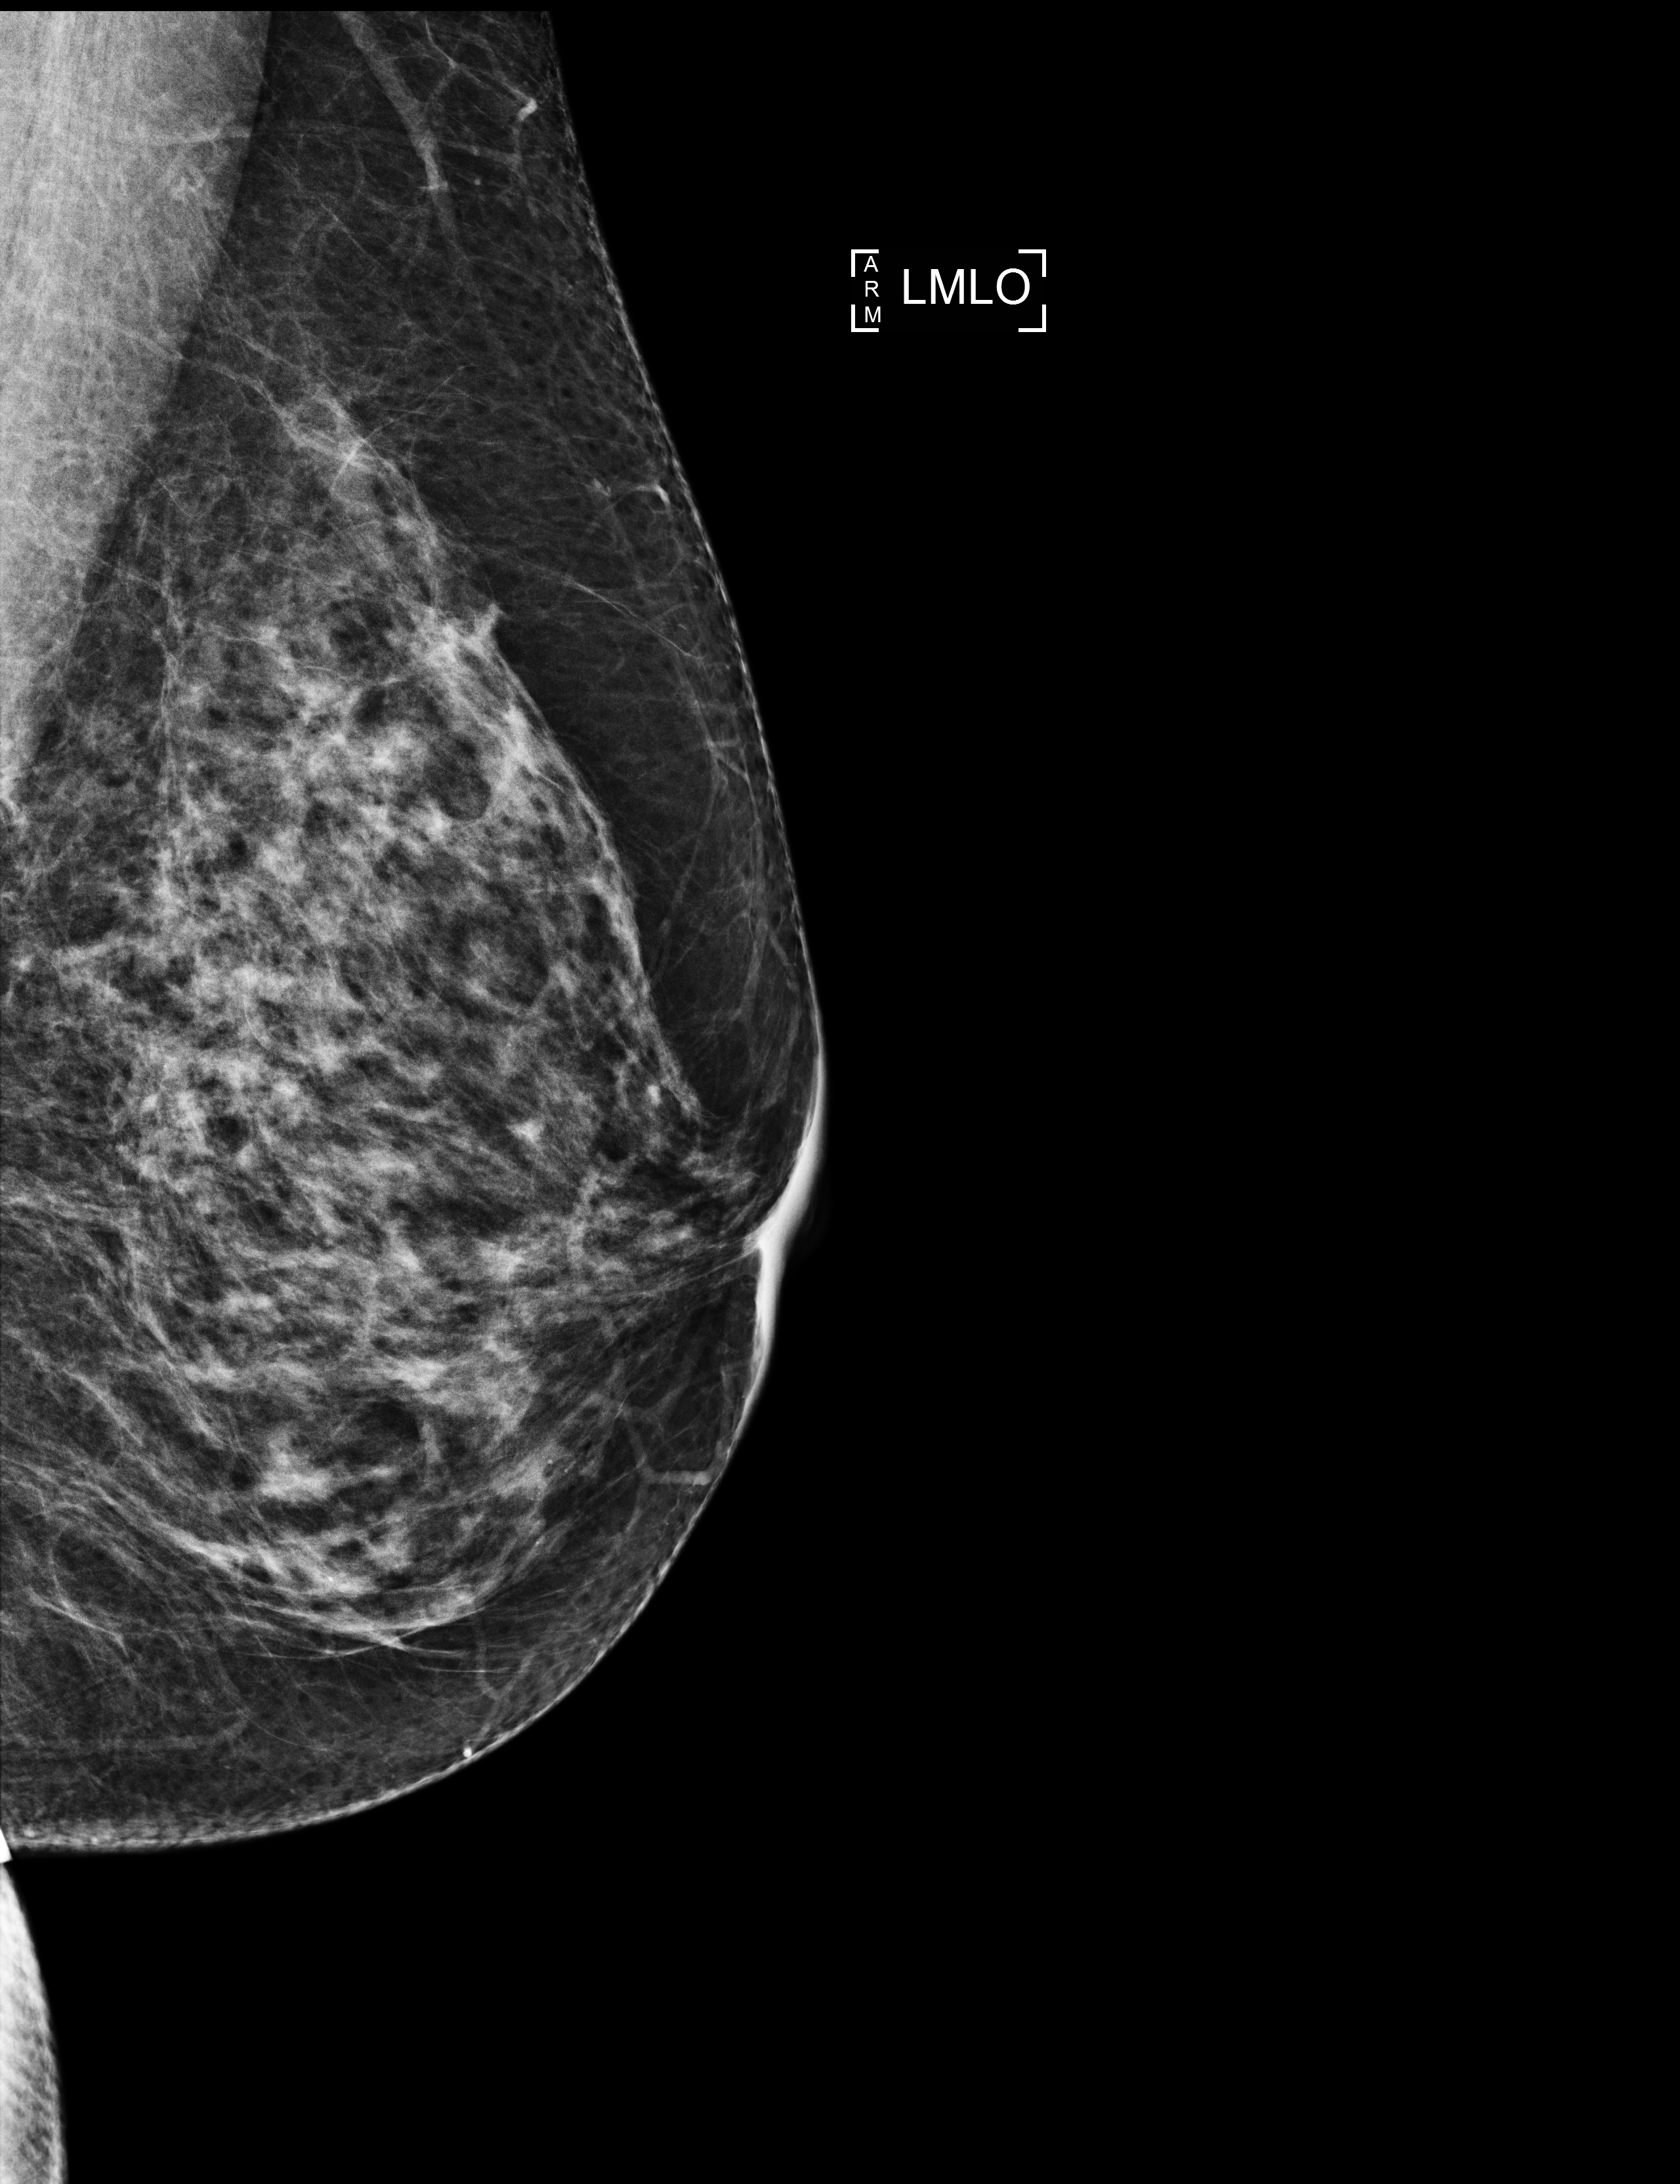
Annual screening mammography examination.
Image type: full-field digital mammogram. Breast: left. Projection: MLO view.